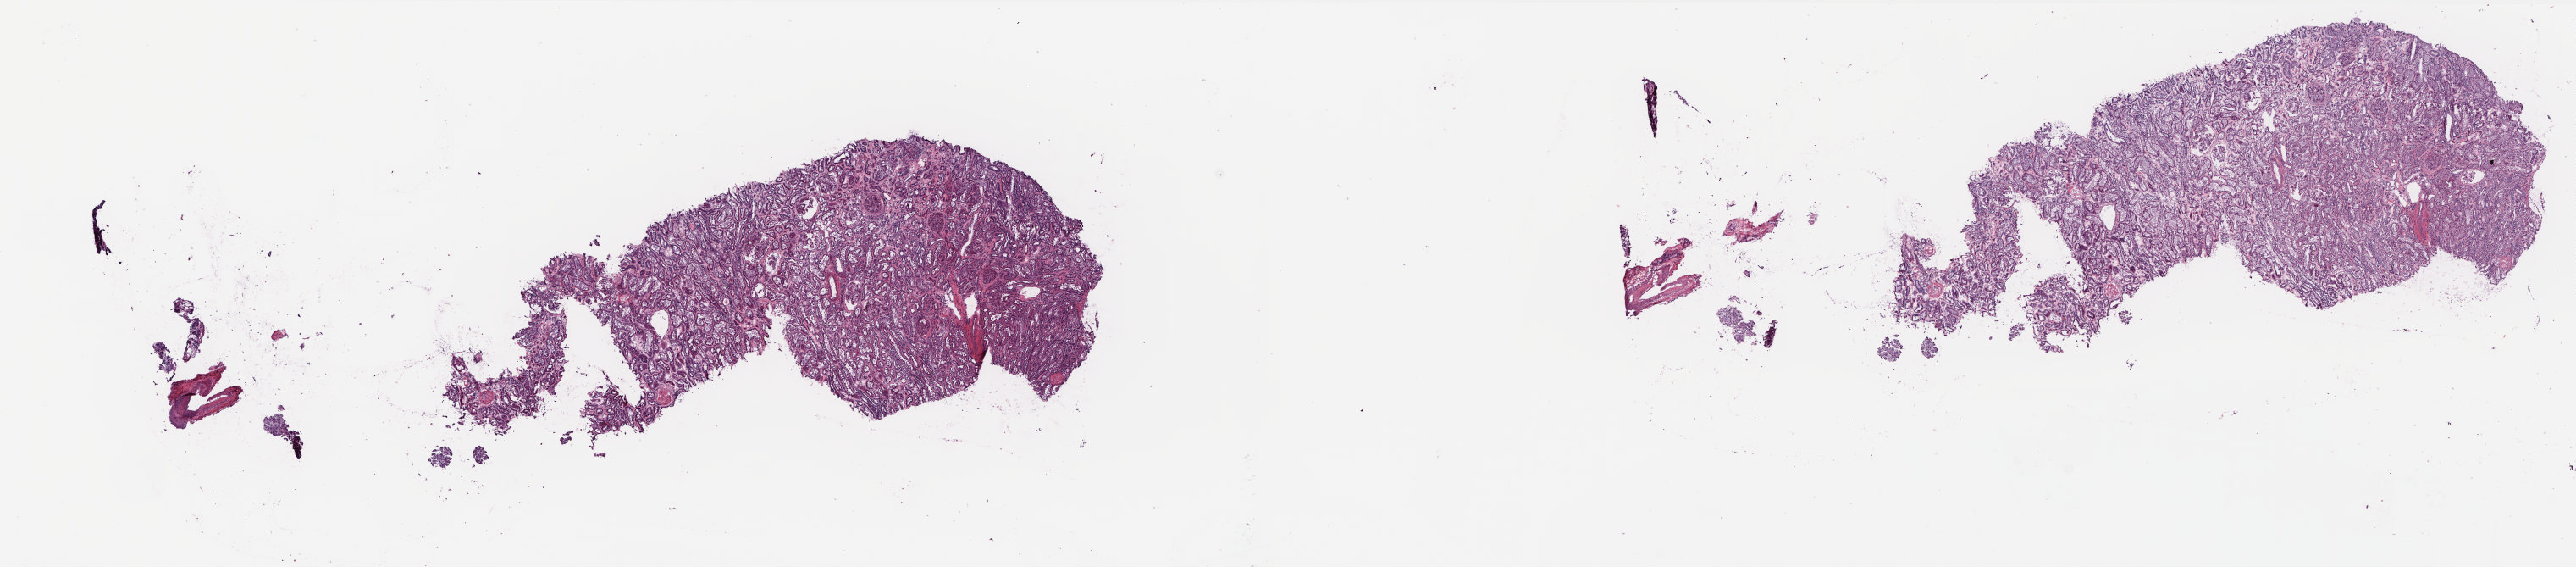
Whole-slide histology image, H&E — whole scanned area (about 24.5 x 5.4 mm, from a 20x scan) shown as a low-resolution overview, frozen section, solid tissue normal (non-tumour tissue) sample from the kidney. Patient: male, age at initial diagnosis 43 years. Pathologist review of this section (percent, as recorded): tumour cells 0%, tumour nuclei 0%, normal cells 65%, stromal cells 35%, necrosis 0%. Infiltration values recorded for this section: lymphocyte infiltration 2%, monocyte infiltration 2%, neutrophil infiltration 0%.
This section: solid tissue normal sample (biorepository sample class). Patient diagnosis: Papillary adenocarcinoma, NOS.